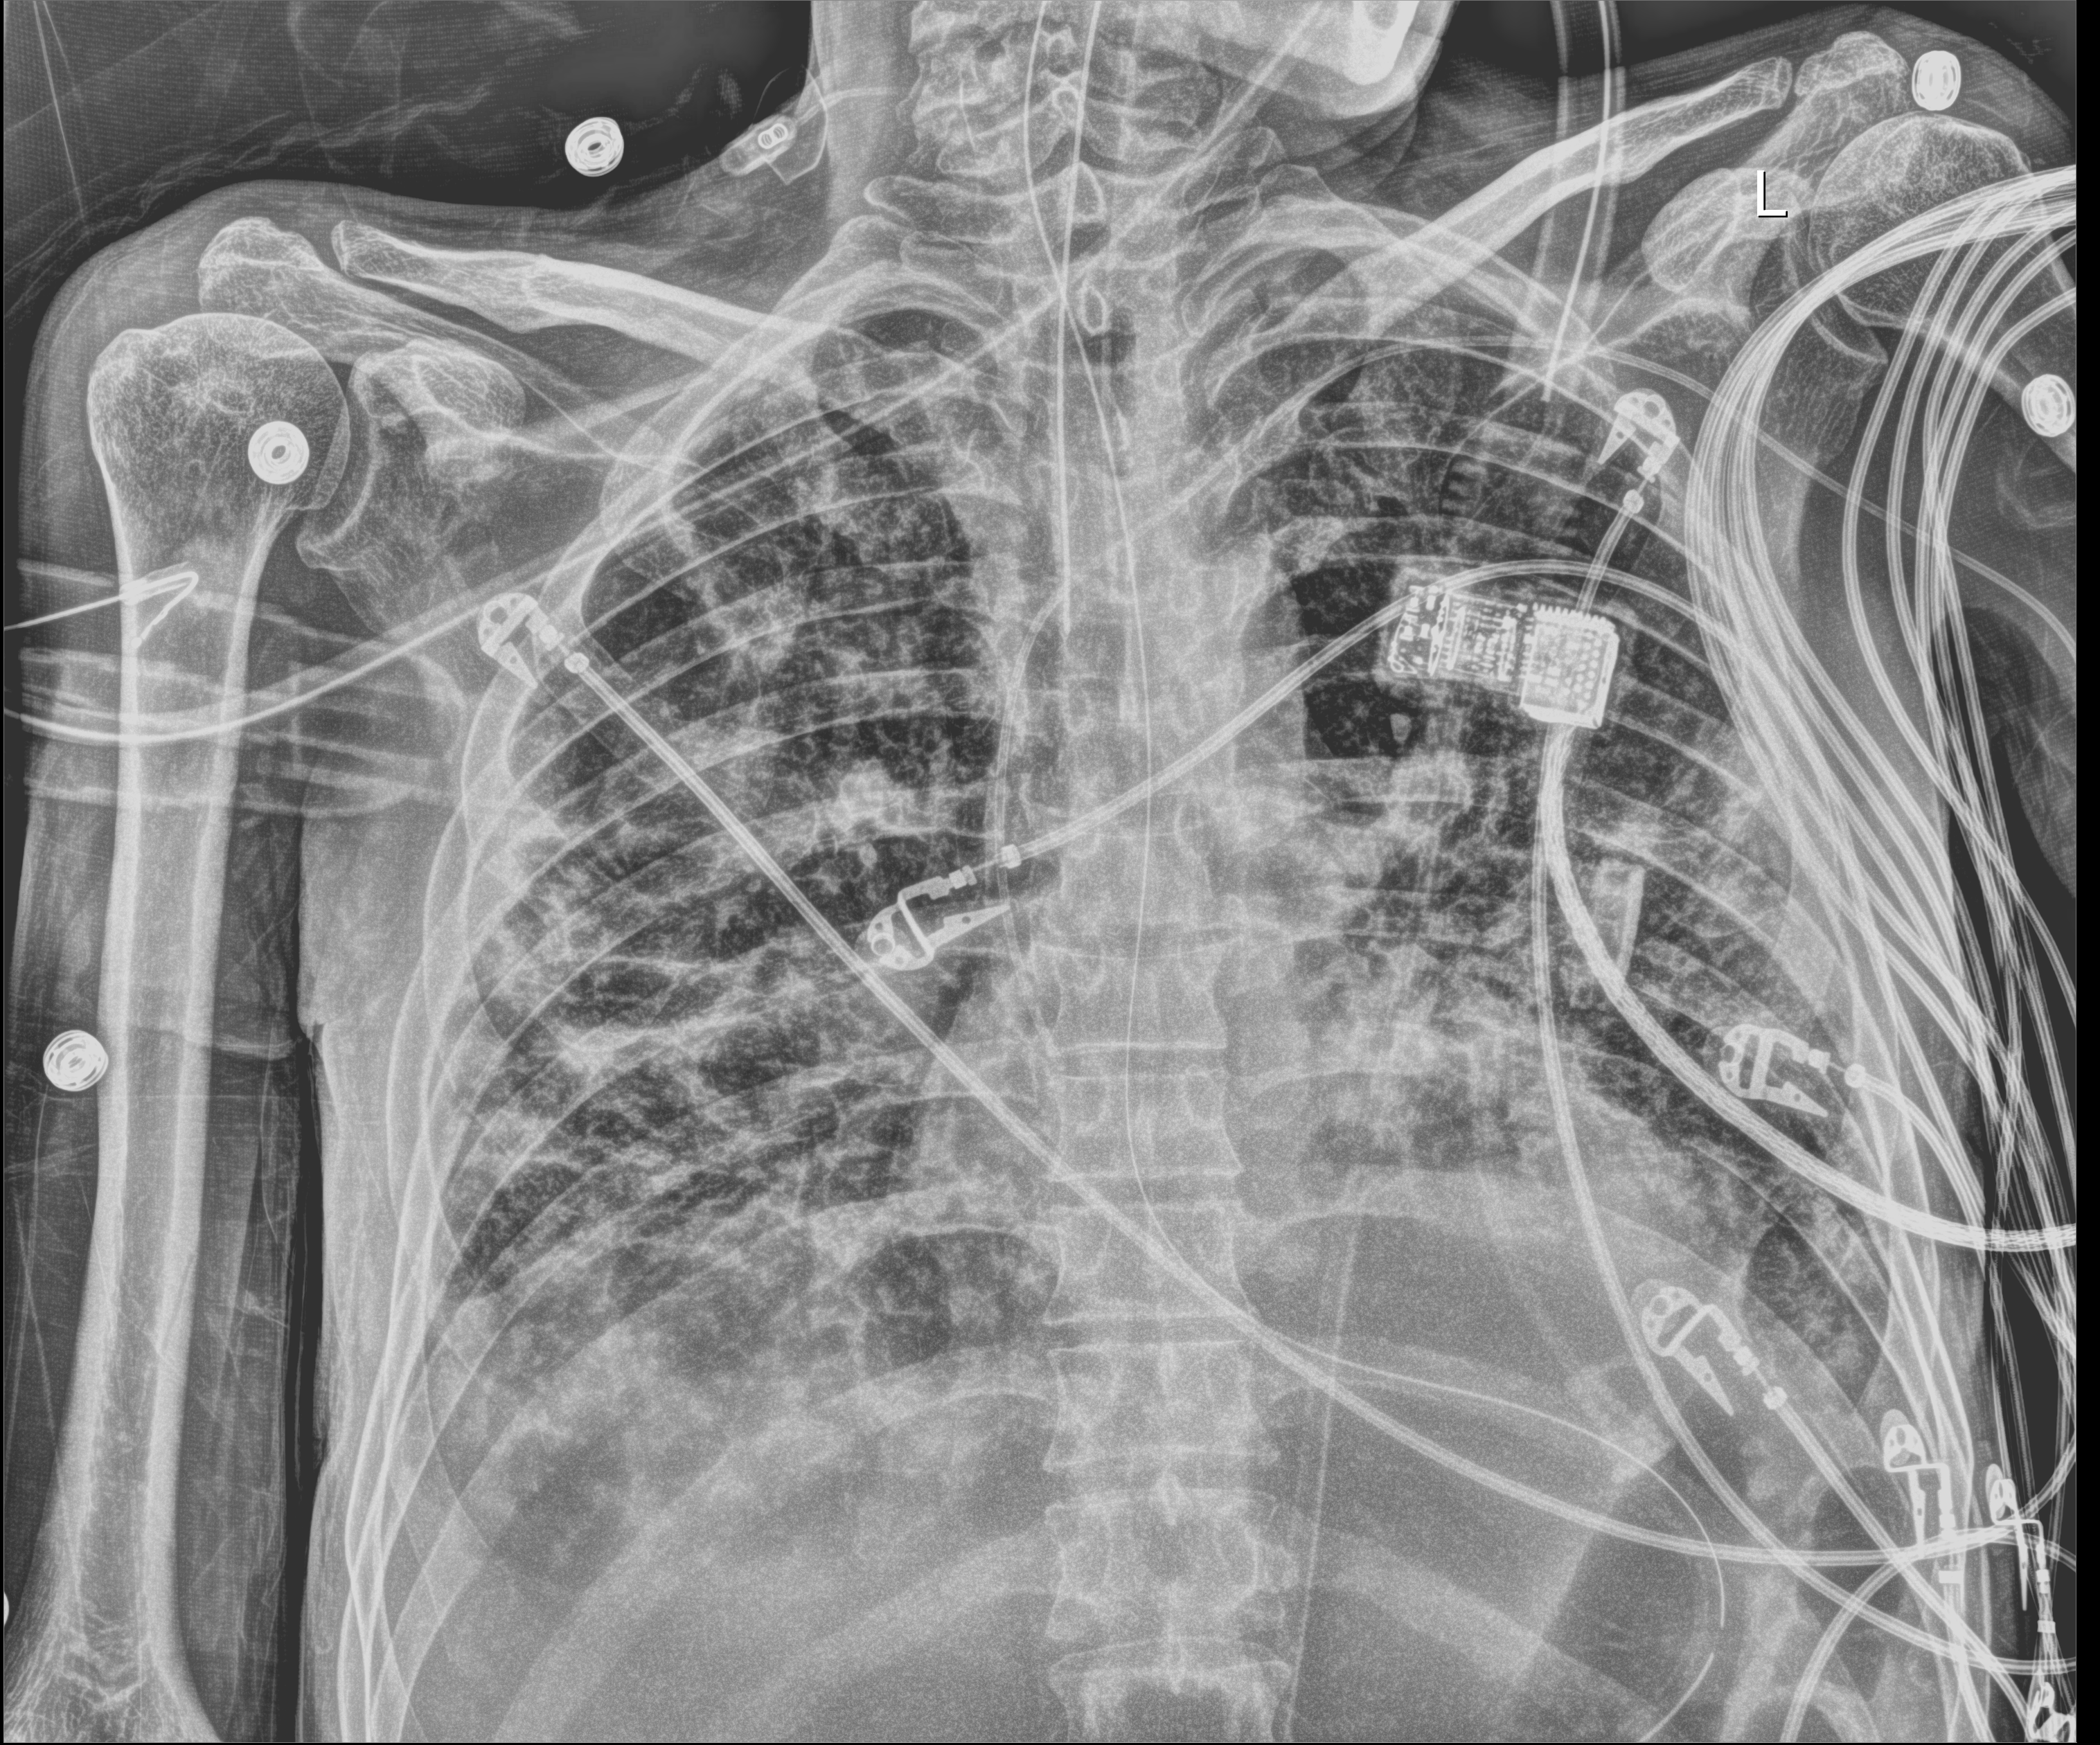
Chest X-ray (portable). Patient hospitalised with COVID-19; male, aged 18–59 years.
Hospital-stay facts (about this admission, not read from this image; timing relative to this image not recorded): admitted to intensive care during this hospital stay: yes; mechanically ventilated during this hospital stay: yes.